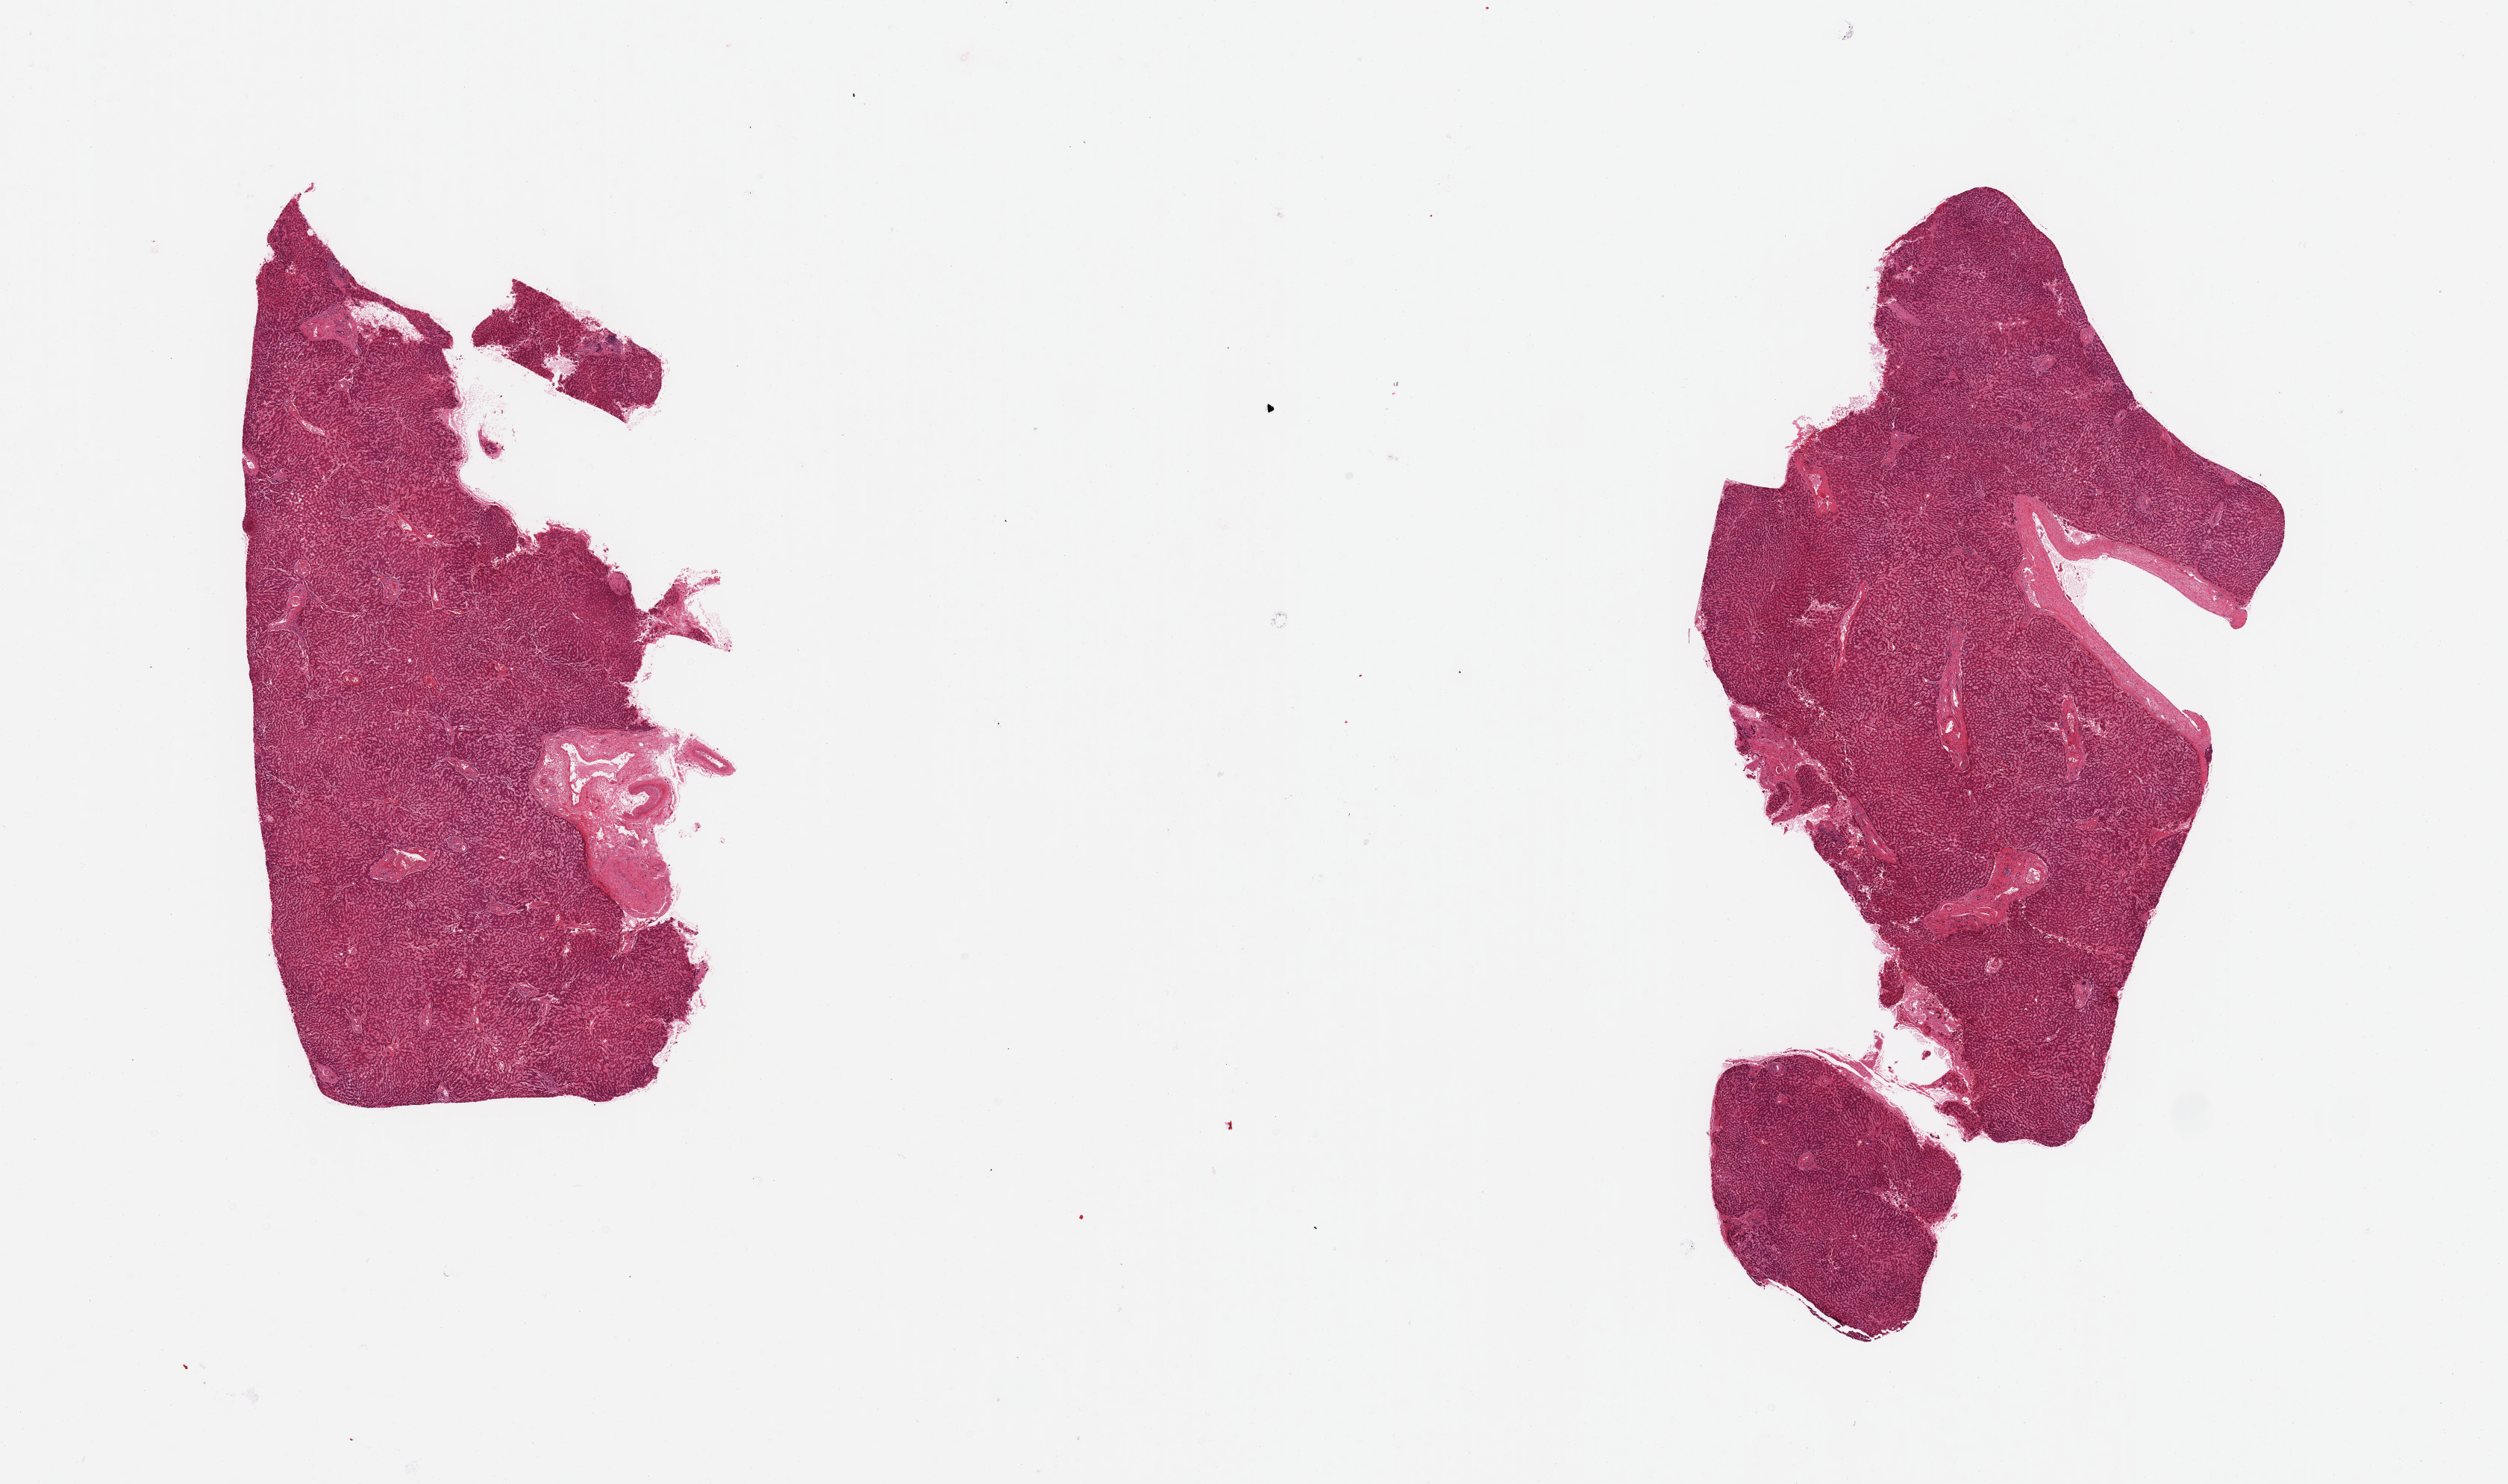
H&E whole-slide image, brightfield, shown as a low-resolution overview of the whole scanned area (about 26.6 x 15.7 mm, acquisition: 20x scan); PAXgene-fixed, paraffin-embedded tissue; section of liver (target tissue); tissue donor sample. Donor sex: male.
Reviewer comment on this tissue sample: 2 pieces, mild congestion.